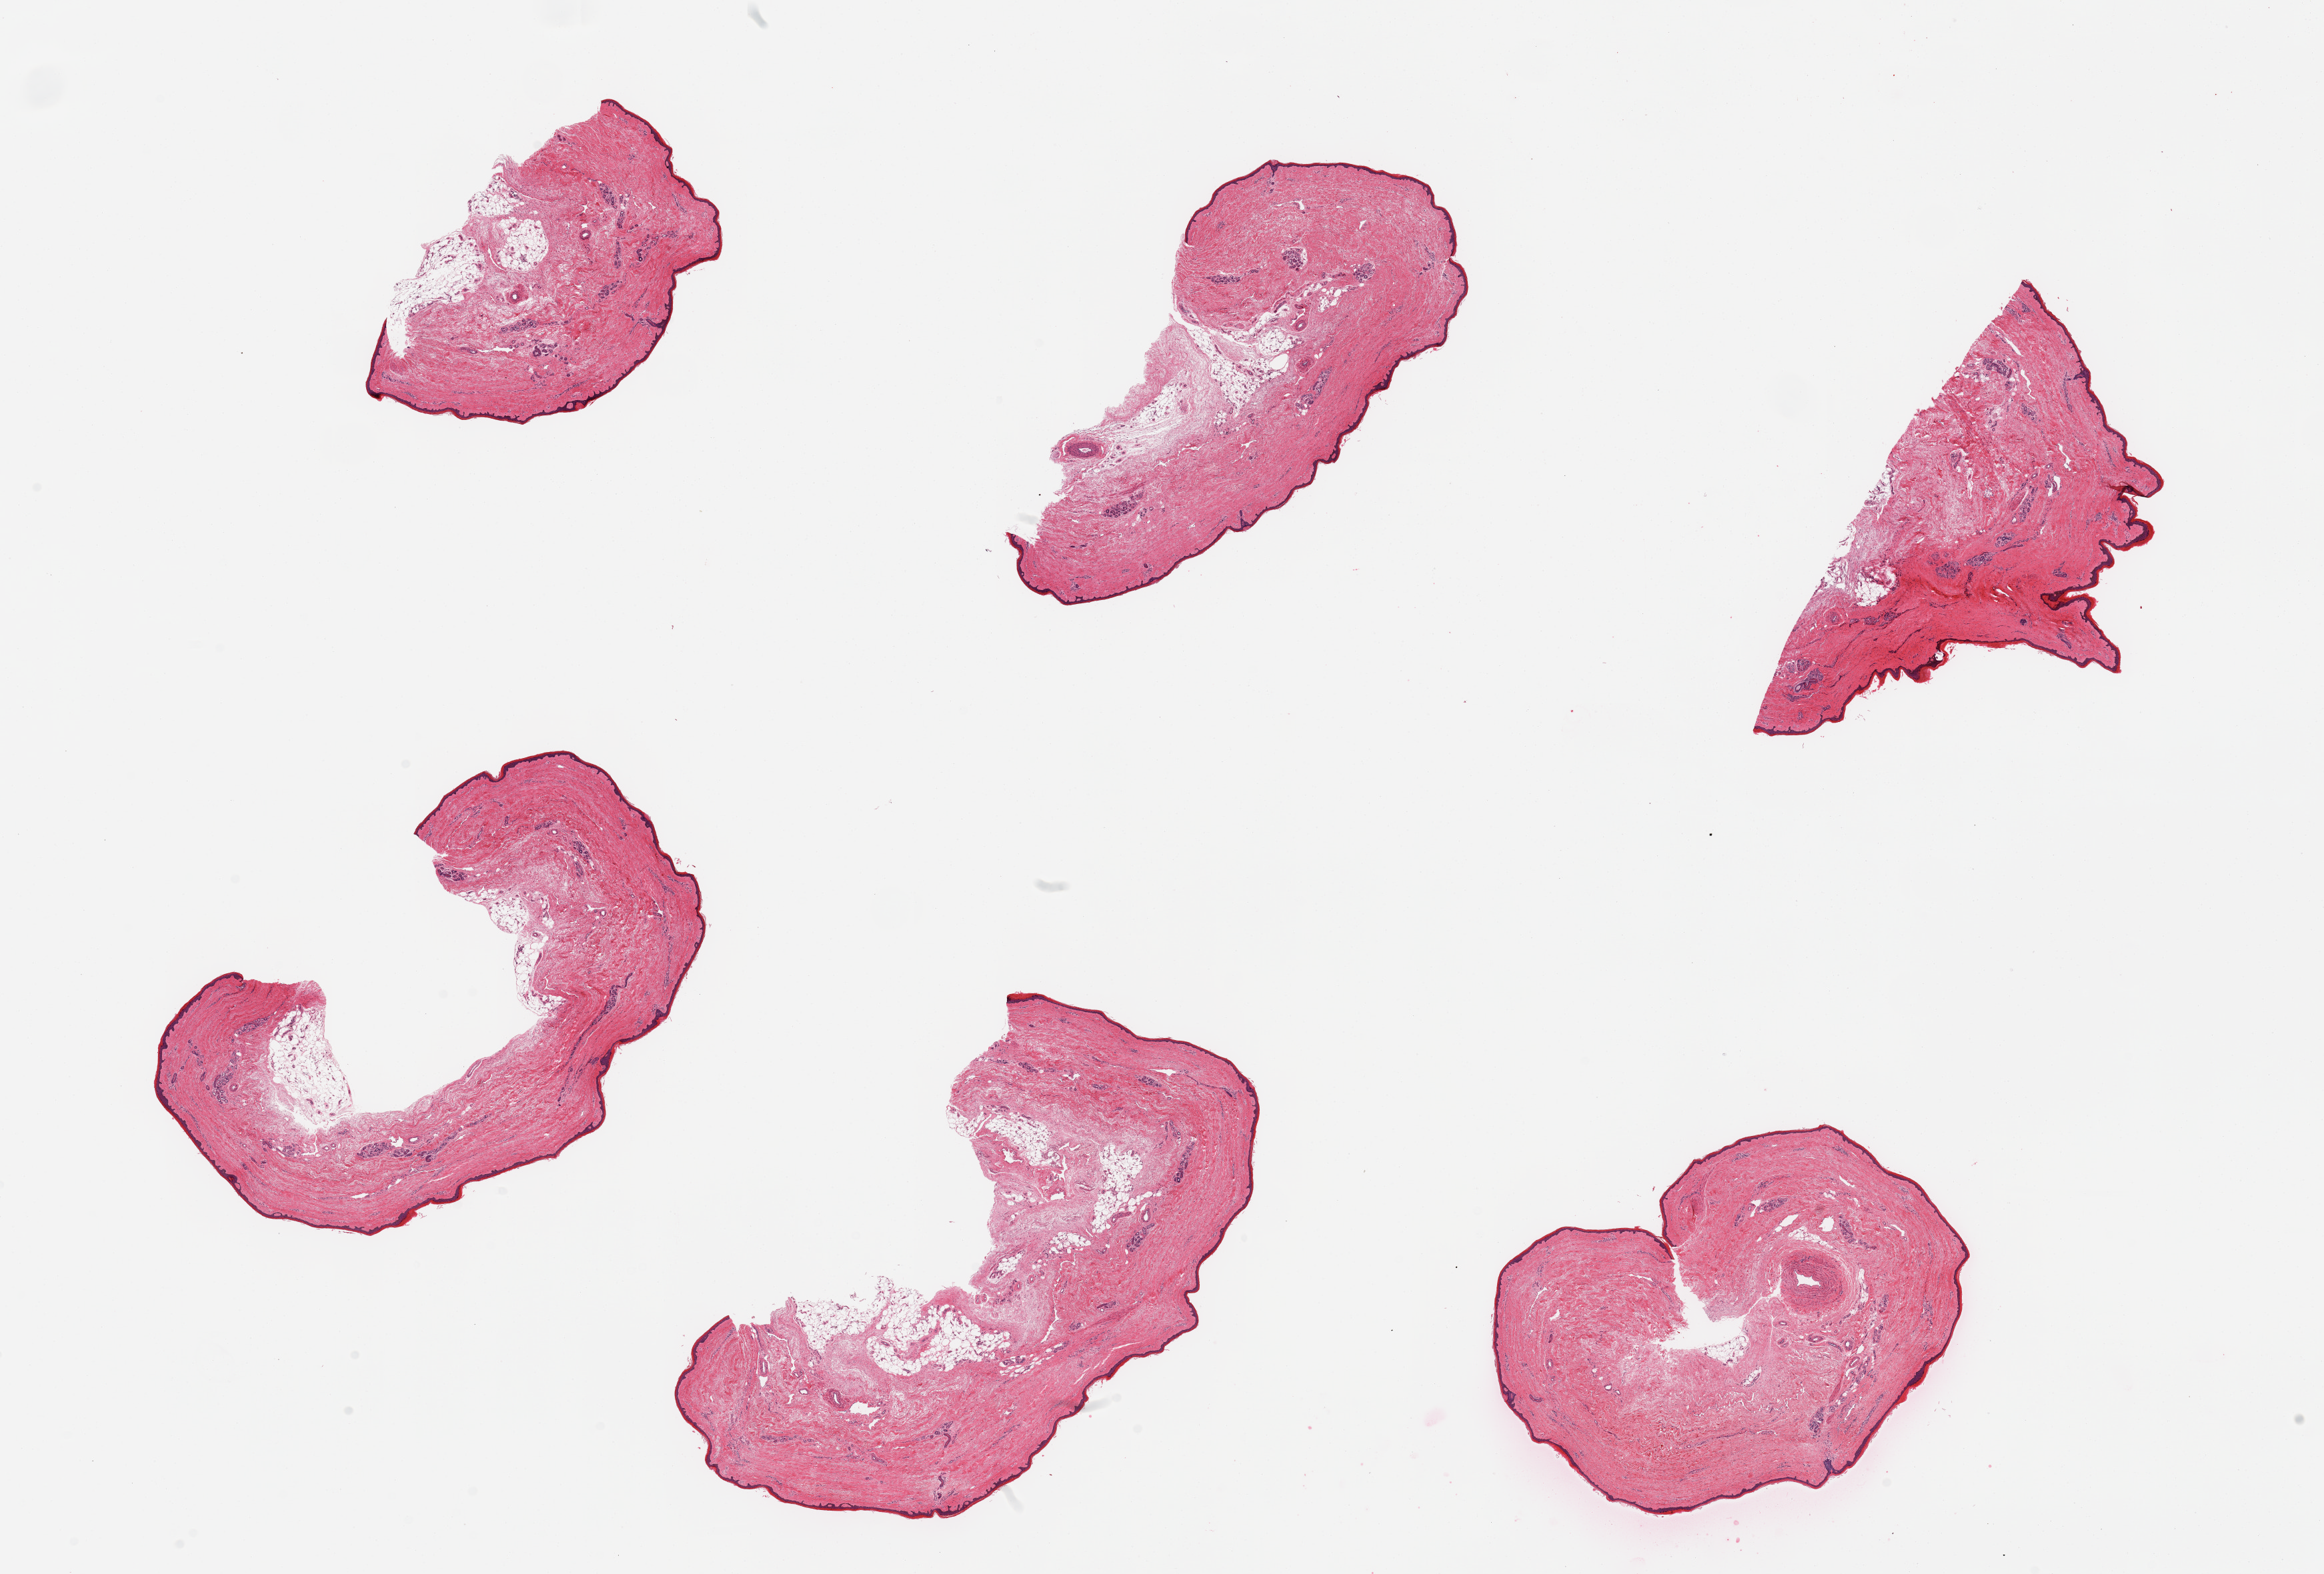
Digitized haematoxylin and eosin-stained section — a low-resolution overview of the entire scanned area, about 27.6 x 18.7 mm (slide scanned at 20x), PAXgene-fixed, paraffin-embedded tissue, target tissue: skin of lower leg, donor tissue sample. Donor: female.
* review note (as recorded): 6 pieces, minimal adherent dermal fat, squamous epithelium is ~30 microns, atrophic